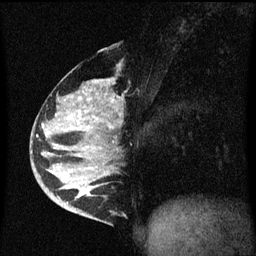
Breast MRI (dynamic contrast-enhanced), one sagittal slice. Position 26 of 60 along the scan axis. Dynamic contrast-enhanced series, image 2 of 3 at this slice position (ordered by acquisition). 1.5 T. TE 4.2 ms, TR 8.4 ms. 256 × 256 image matrix, field of view 200 × 200 mm. Patient: female, 34 years. From the clinical record (not read from this slice): setting: breast cancer imaged before/during neoadjuvant chemotherapy; receptor status: HR-positive, HER2-negative.
Annotated regions visible in this slice (semi-automatically segmented with operator editing):
- analysis volume of interest (the breast-tissue region the enhancement analysis was run in; not a lesion): box from (x=34, y=48) to (x=121, y=215) px
- tumour enhancement mask (voxels above the 70 % enhancement threshold inside the analysis volume of interest): (x=62, y=80)–(x=103, y=197)